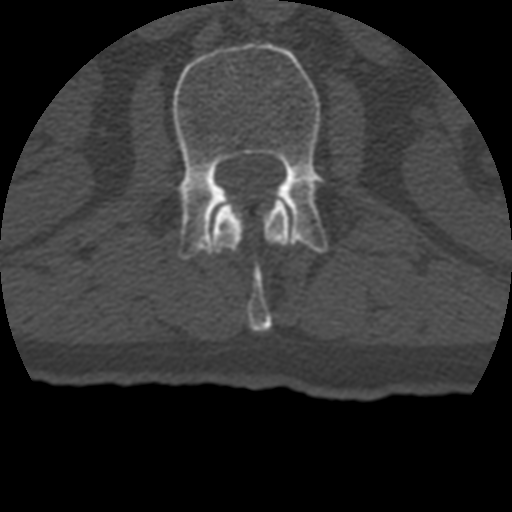
CT including the spine, one axial slice. Position 126 of 399 along the scan axis. Reconstruction kernel STANDARD. 120 kVp. Bone window (W 1800 / L 400 HU). 1.25 mm slice thickness. 512 × 512 image matrix, field of view 160 × 160 mm. Patient age 69 years. Case-level facts recorded for this patient, not image findings: primary cancer: prostate.
Structures marked on this image (semi-automatically segmented with operator editing):
- L1 vertebra: box from (x=212, y=198) to (x=292, y=332) px
- L2 vertebra: (x=173, y=42)–(x=328, y=259)